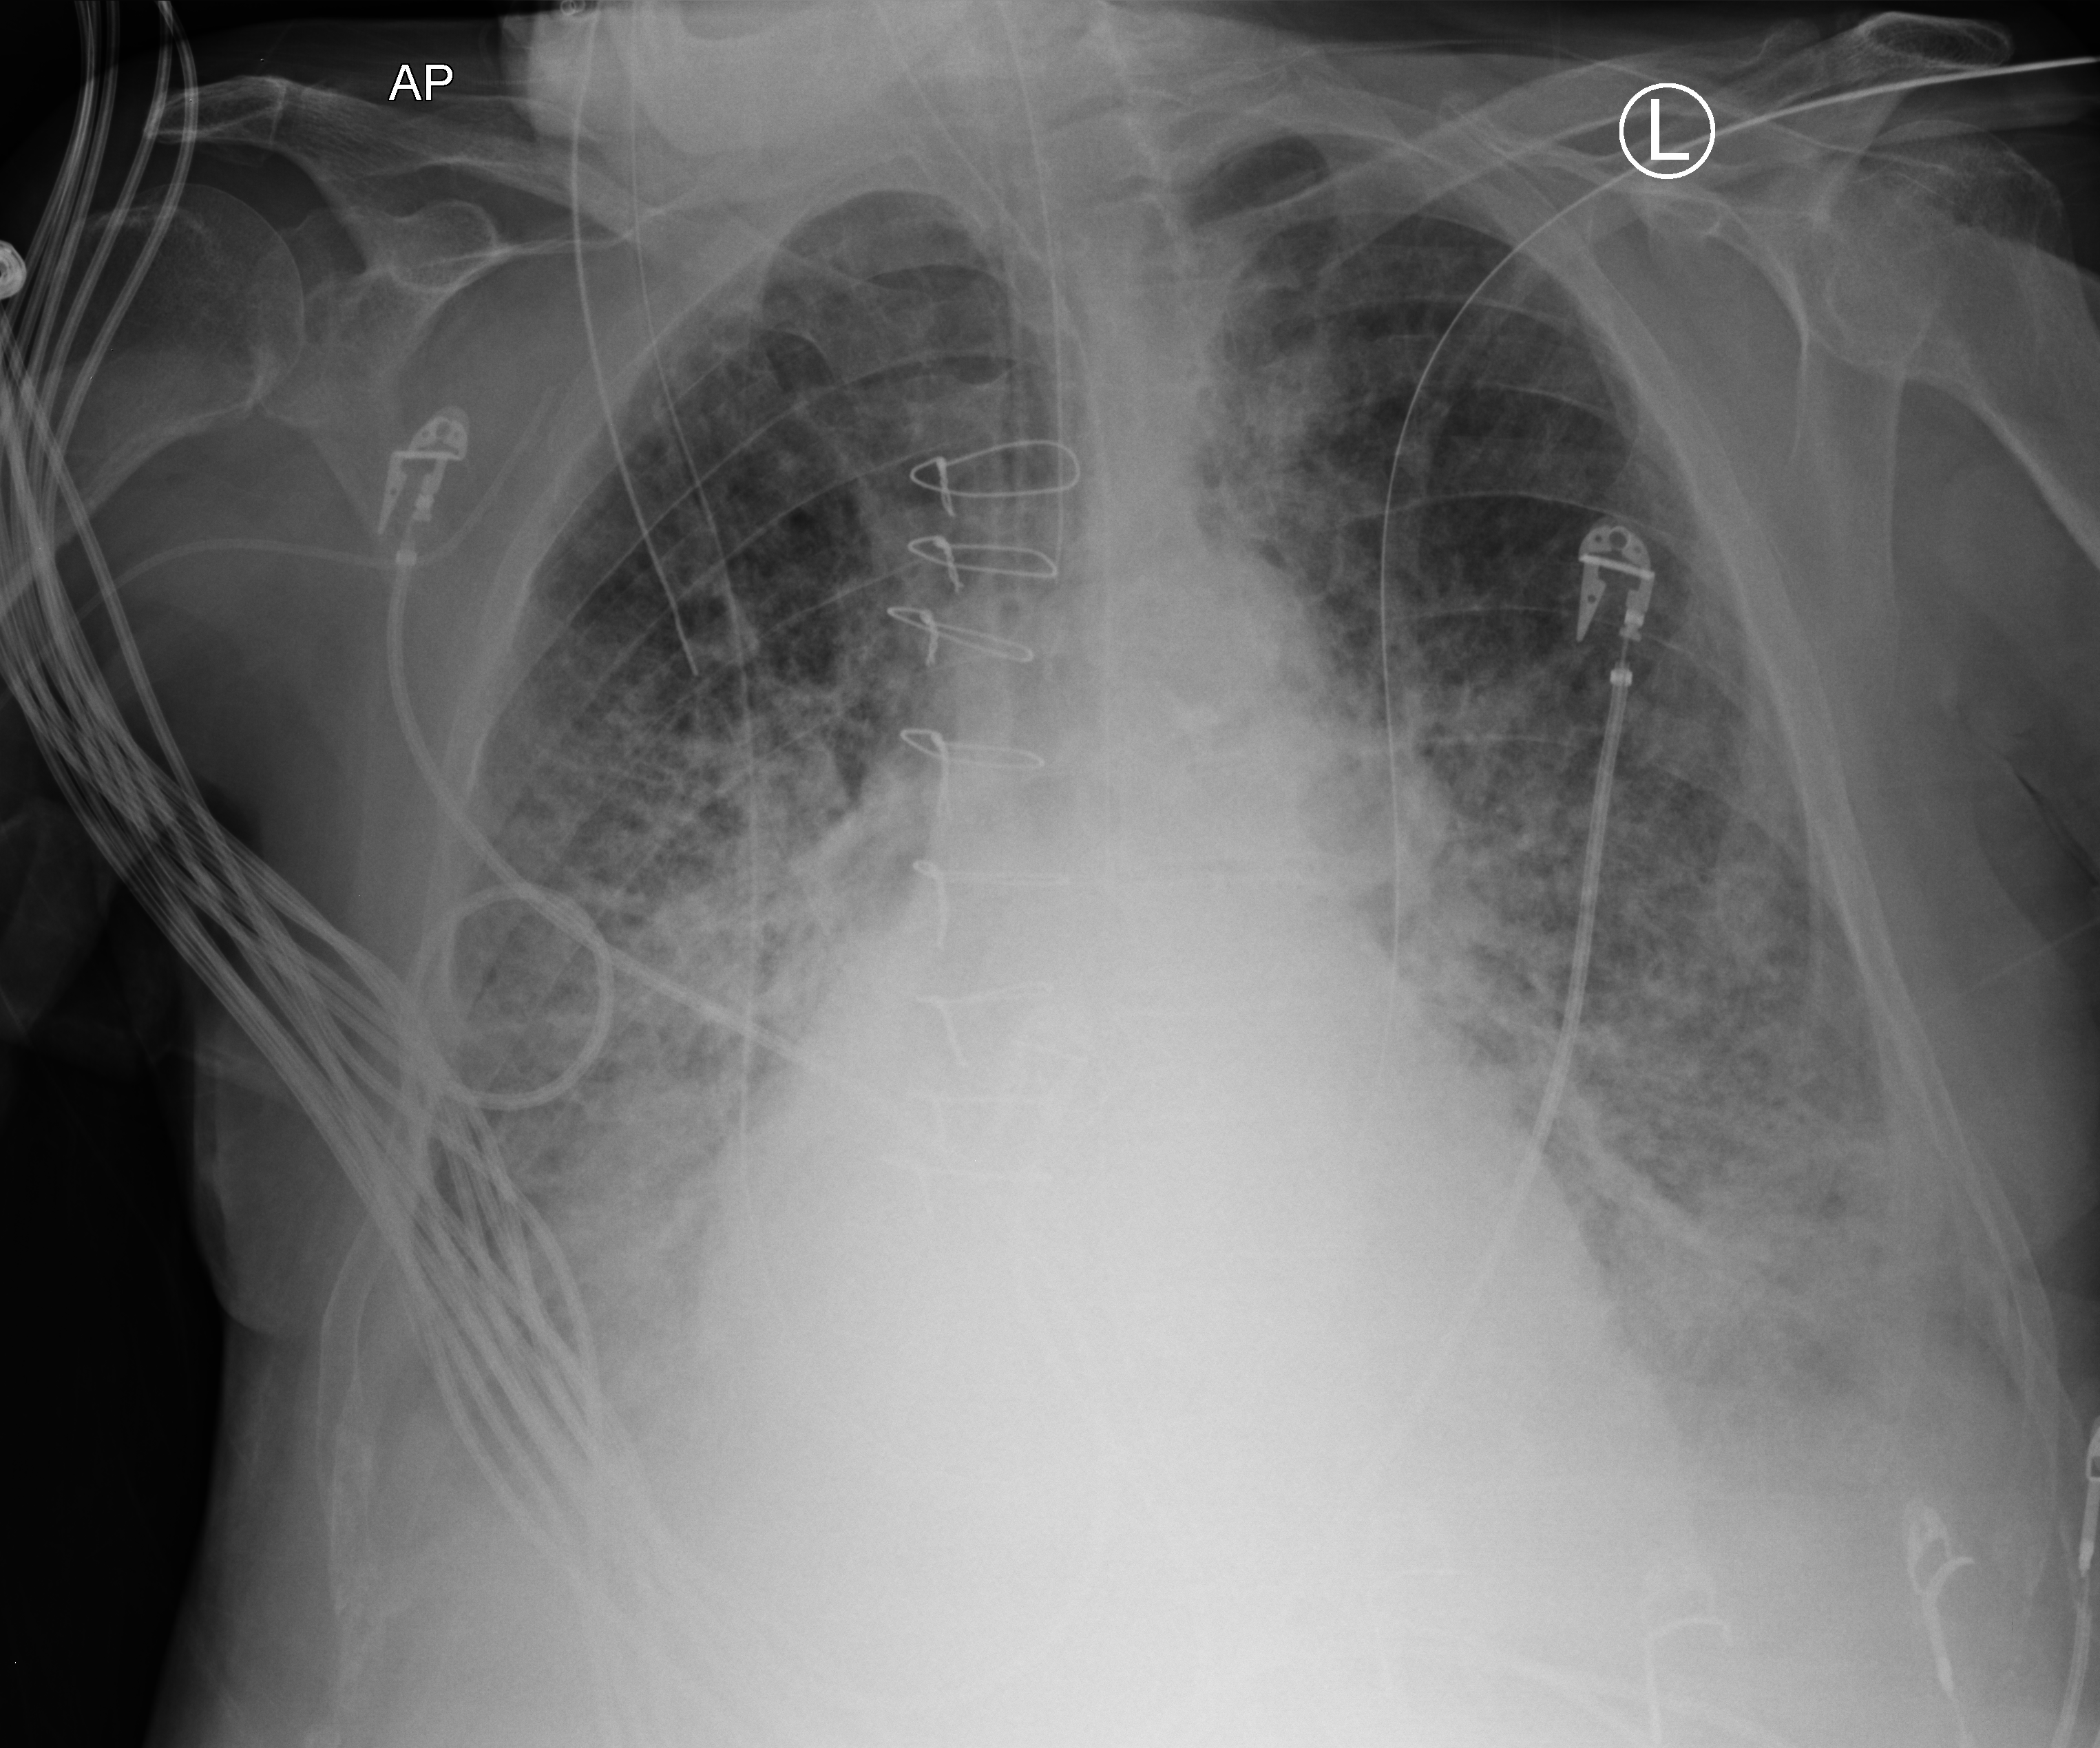
Portable chest radiograph, anteroposterior (AP) projection. Patient hospitalised with COVID-19; male, aged 75–90 years.
Admission-level facts for this patient (not findings on this image; timing relative to this image not recorded): admitted to intensive care during this hospital stay: yes.